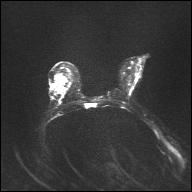
Breast MRI, one axial slice. Position 19 of 32 along the scan axis. Diffusion-weighted series; image 2 of 4 stored at this slice position (different b-values; order by instance number). 1.5 T. 4 mm slice thickness. 192 × 192 image matrix, field of view 360 × 360 mm. Female patient.
Outlined on this slice (manually delineated by an expert):
- tumour on diffusion-weighted imaging: box from (x=56, y=75) to (x=65, y=93) px